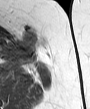
MRI of an extremity soft-tissue mass, one axial slice; slice 27 of 45 in the series (ordered by position); MR volume resampled by the dataset authors to the PET/CT grid (not the native acquisition matrix); 90 × 109 image matrix, field of view 88 × 106 mm. Female patient. From the clinical record (not read from this slice): histological type: leiomyosarcoma; grade: intermediate; site of the primary tumour: parascapusular.
Structures marked on this image (expert contour drawn on MRI and transferred to this co-registered scan by the dataset authors):
- gross tumour volume including surrounding oedema: bounding box (x1, y1, x2, y2) in pixels: (21, 29, 45, 49)
- gross tumour volume (mass): (23, 30, 38, 45)